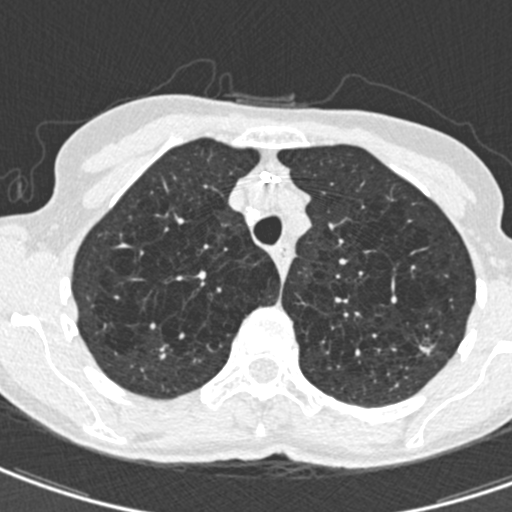
Axial slice from a low-dose chest CT screening exam. Second screening round (one year after baseline). Lung window (W 1500 / L -600 HU). 120 kVp. Slice 121 of 498 in the series. Female, age 71 years at enrolment. Current smoker at enrolment.
• Lesion marked by an expert reader, bounding box [x1, y1, x2, y2] px = [404, 331, 444, 369].
• The screening reader recorded 2 non-calcified nodules or masses ≥4 mm on this exam; which of them this box marks is not recorded.
• Official screen result: positive, change unspecified: nodule(s) >= 4 mm or enlarging nodule(s), mass(es), or other non-specific abnormalities suspicious for lung cancer.
• Later outcome: lung cancer diagnosed 604 days after this screen (after the third annual screen) — adenocarcinoma, NOS, left upper lobe, moderately differentiated (G2), stage IA (AJCC 6th edition), 12 mm at pathology.